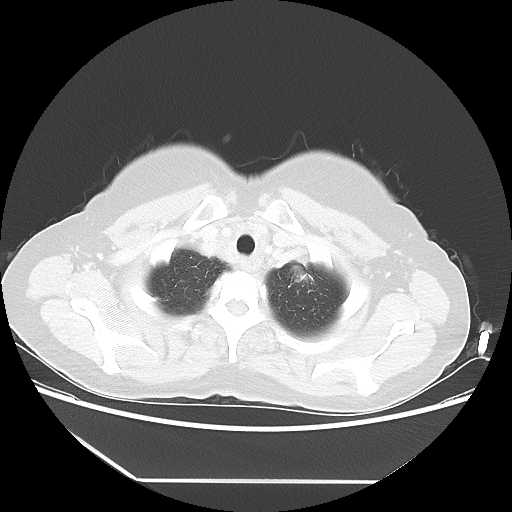
Chest CT, one axial slice; position 47 of 52 along the scan axis; 100 kVp; lung window (W 1500 / L -600 HU); 5 mm slice thickness; 512 × 512 image matrix, field of view 390 × 390 mm. Female patient, age 50 years. From the clinical record (not read from this slice): clinical TNM (as recorded): T2 N3 M0.
Annotated regions visible in this slice (rectangle marked by the reading radiologist):
- lung tumour (recorded histology: adenocarcinoma): bounding box [x1, y1, x2, y2] px = [288, 254, 315, 287]